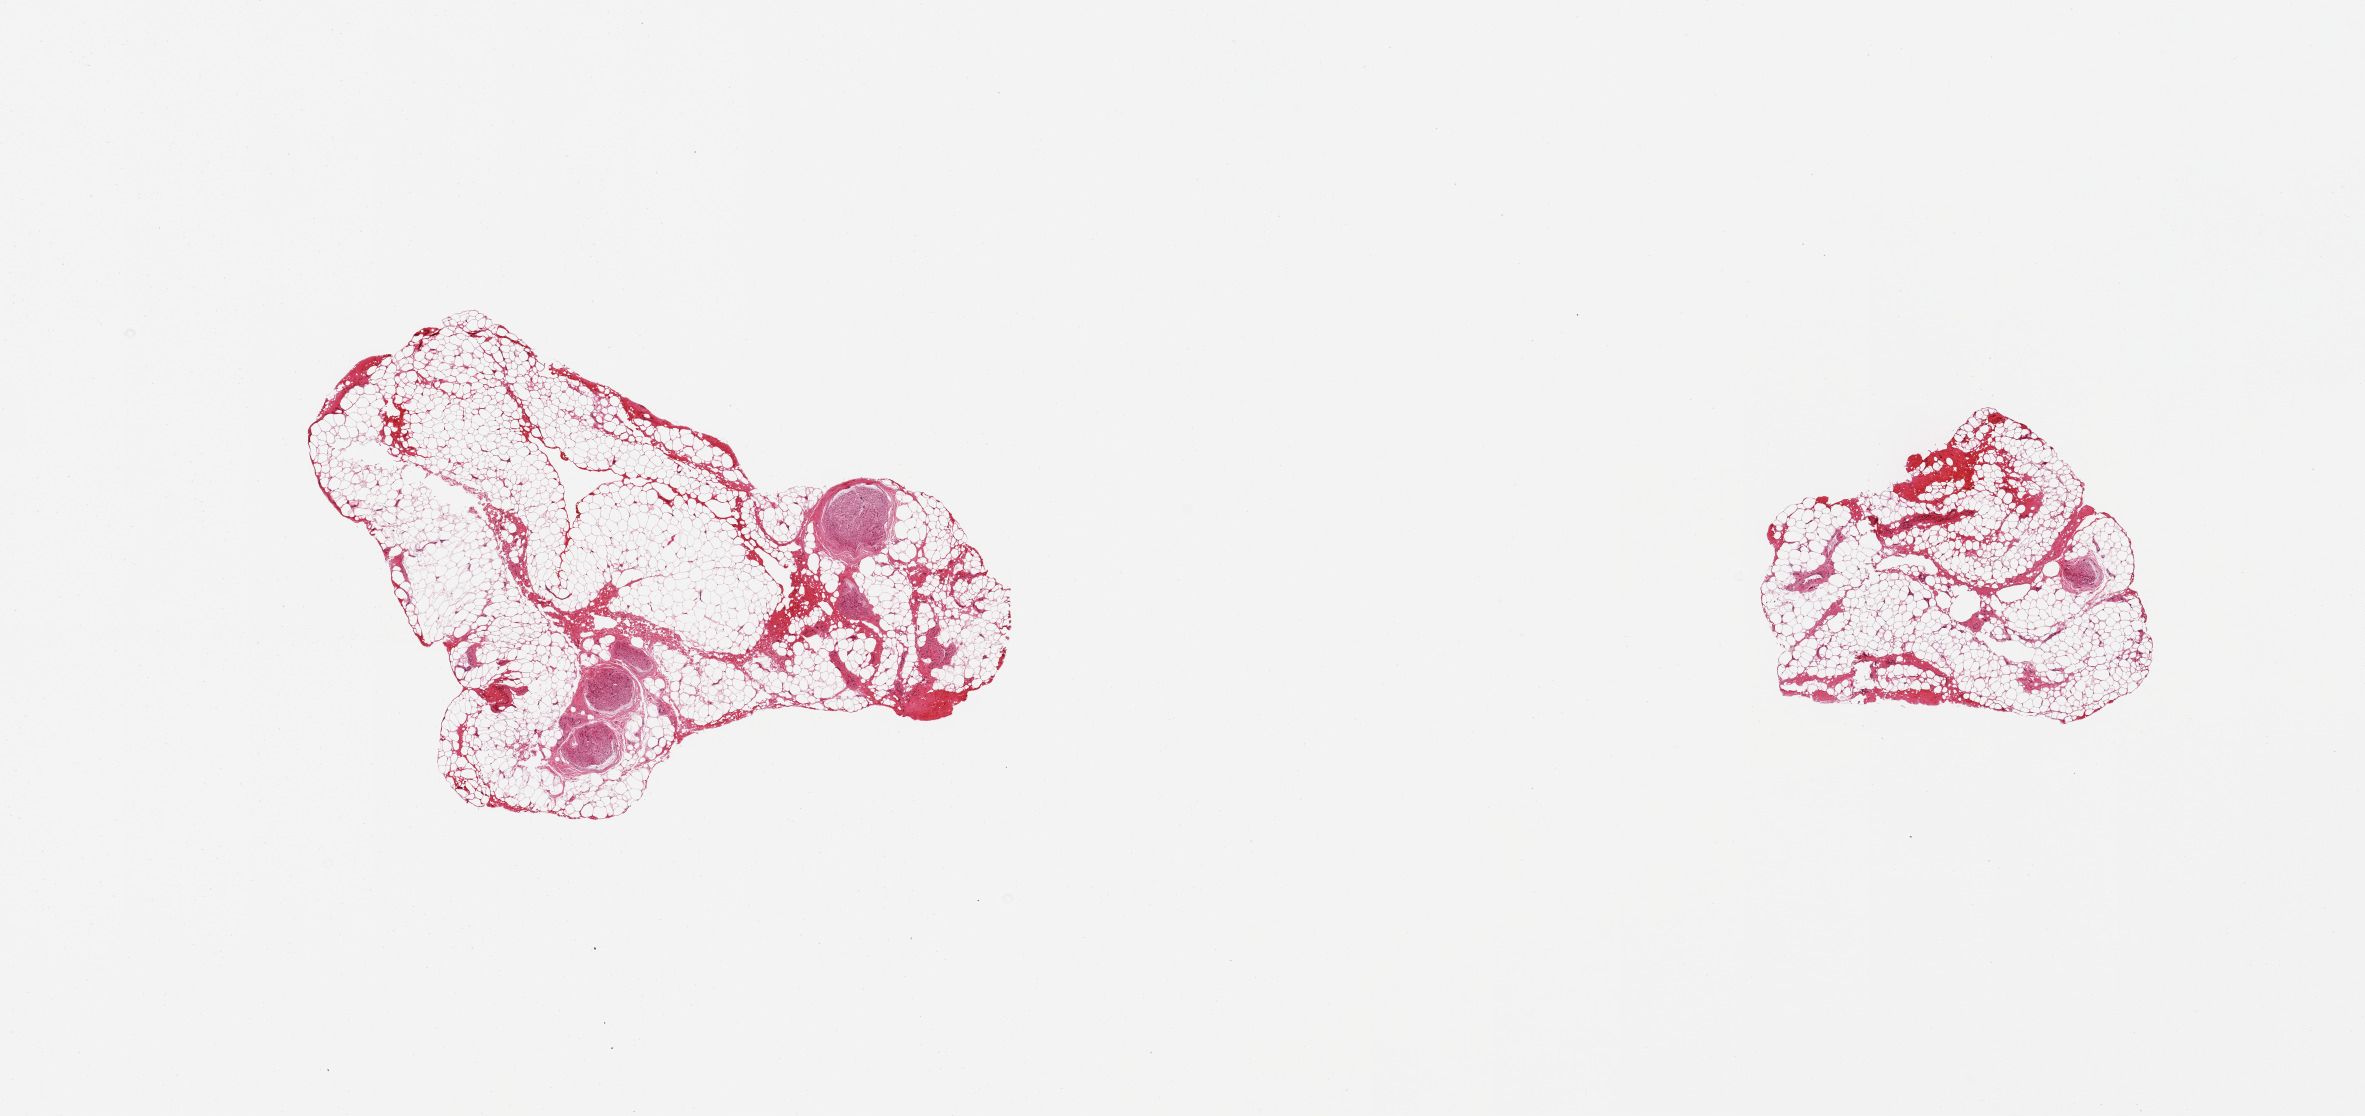
Haematoxylin and eosin whole-slide image — whole scanned area (about 18.7 x 8.8 mm) shown as a low-resolution overview. PAXgene-fixed, paraffin-embedded tissue. Sampled site (target tissue): tibial nerve. Donor tissue sample. Donor sex: male.
Reviewer comment on this tissue sample: 2 pieces: >90% fat; several nerve fibers marked.